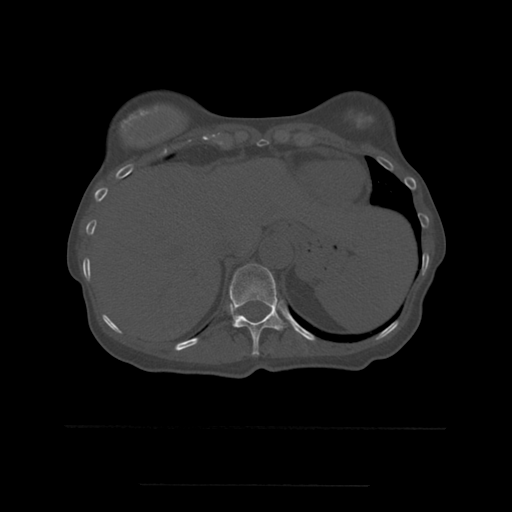
CT including the spine, one axial slice. Position 280 of 544 along the scan axis. Bone window (W 1800 / L 400 HU). 1.25 mm slice thickness. 512 × 512 image matrix. Patient age 58 years. From the clinical record (not read from this slice): primary cancer: lung.
Structures marked on this image (semi-automatic segmentation, software-assisted and operator-edited):
- T11 vertebra: bounding box <230,264,285,355> (left, top, right, bottom; pixels)